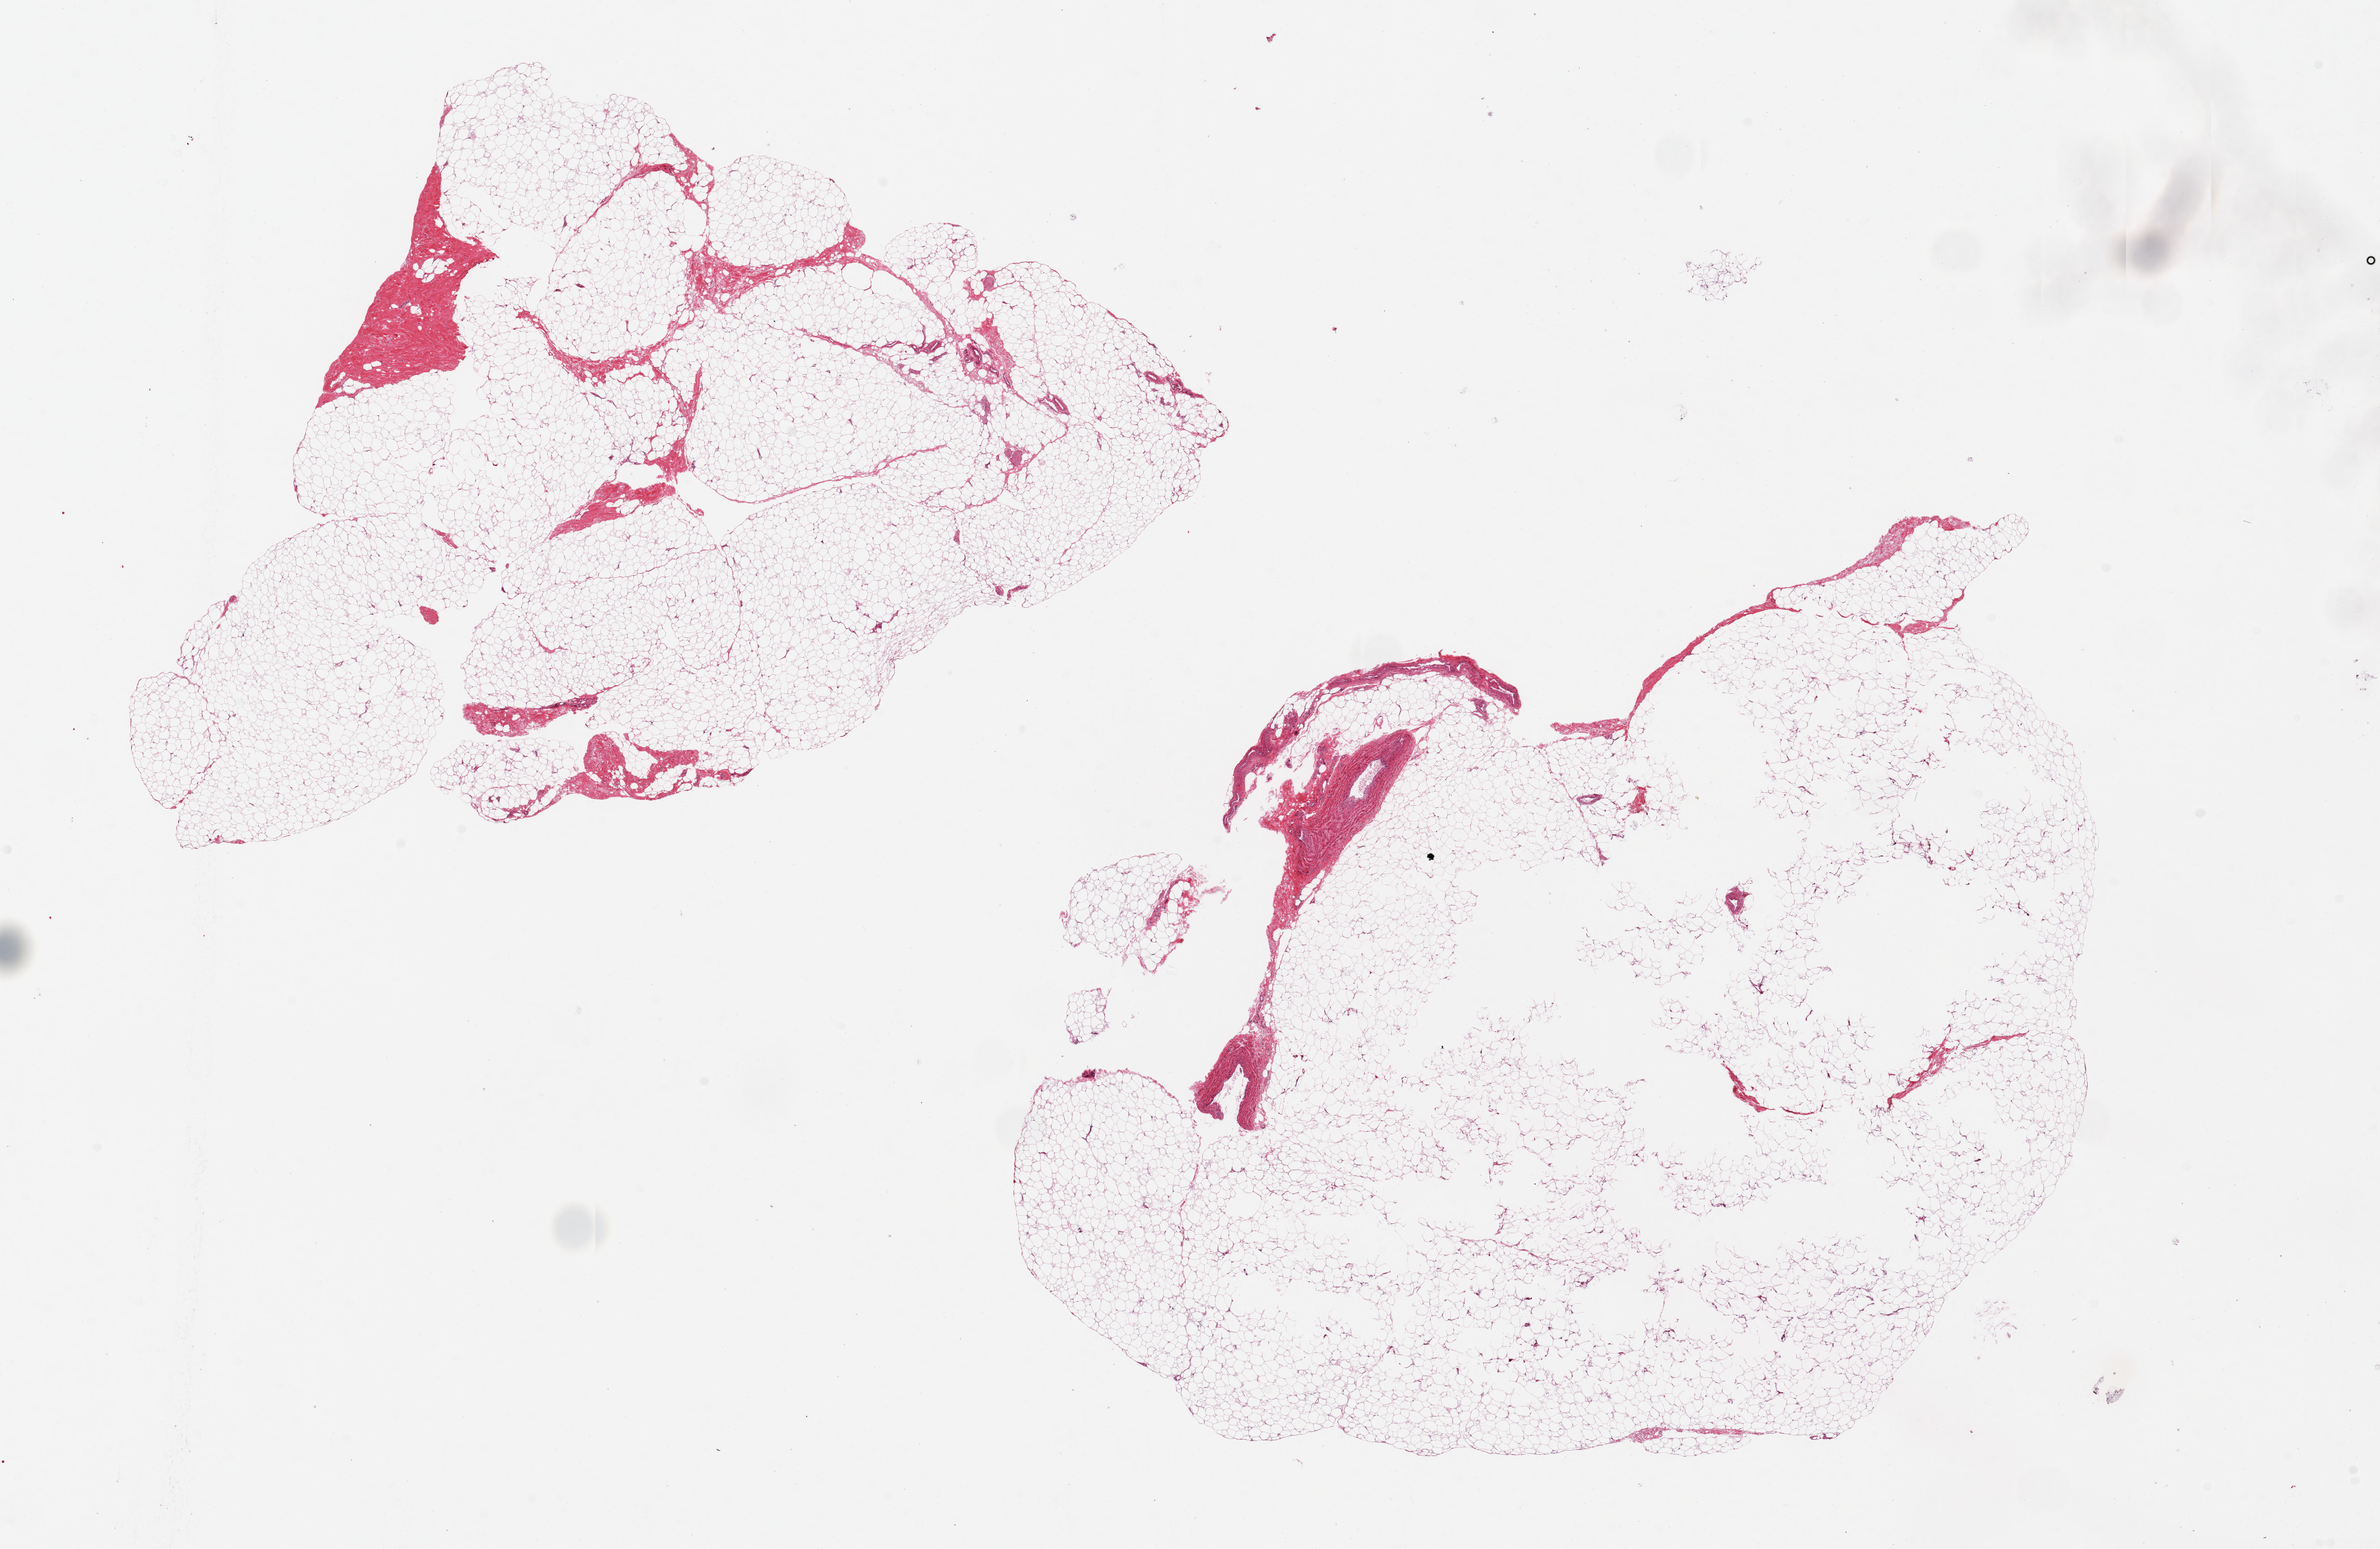
Digitized haematoxylin and eosin-stained section, low-resolution overview of the scanned area, about 27.6 x 17.9 mm (acquisition: 20x scan); PAXgene-fixed, paraffin-embedded tissue; sampled site (target tissue): adipose tissue; tissue donor sample. Donor: male.
Pathologist's review note for this sample: 2 pieces ~10x10mm.